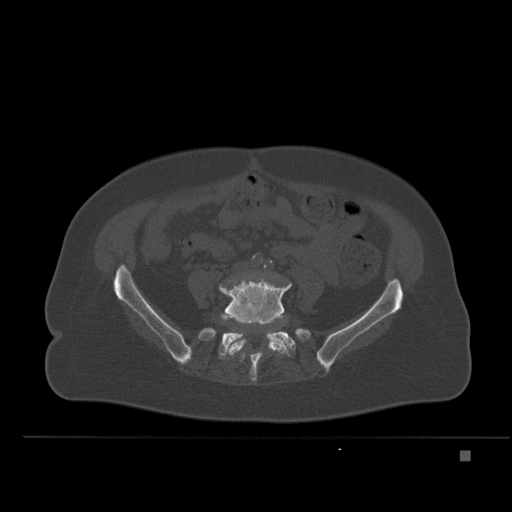
CT including the spine, one axial slice; position 158 of 477 along the scan axis; bone window (W 1800 / L 400 HU); 1.5 mm slice thickness; 512 × 512 image matrix. Female patient, age 74 years. From the clinical record (not read from this slice): primary cancer: colon.
Annotated regions visible in this slice (semi-automatically segmented with operator editing):
- L5 vertebra: bounding box [x1, y1, x2, y2] px = [218, 277, 292, 356]